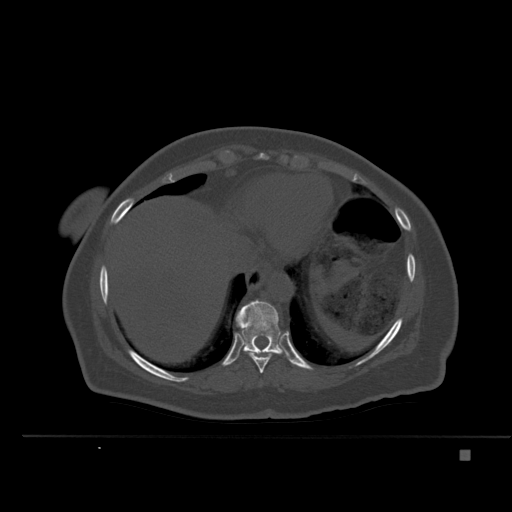
CT including the spine, one axial slice; position 289 of 477 along the scan axis; bone window (W 1800 / L 400 HU); 512 × 512 image matrix, field of view 422 × 422 mm. Patient: female, 74 years. From the clinical record (not read from this slice): primary cancer: colon.
Structures marked on this image (semi-automatically segmented with operator editing):
- T10 vertebra: bounding box (x1, y1, x2, y2) in pixels: (236, 300, 285, 355)
- T9 vertebra: (240, 326, 276, 373)